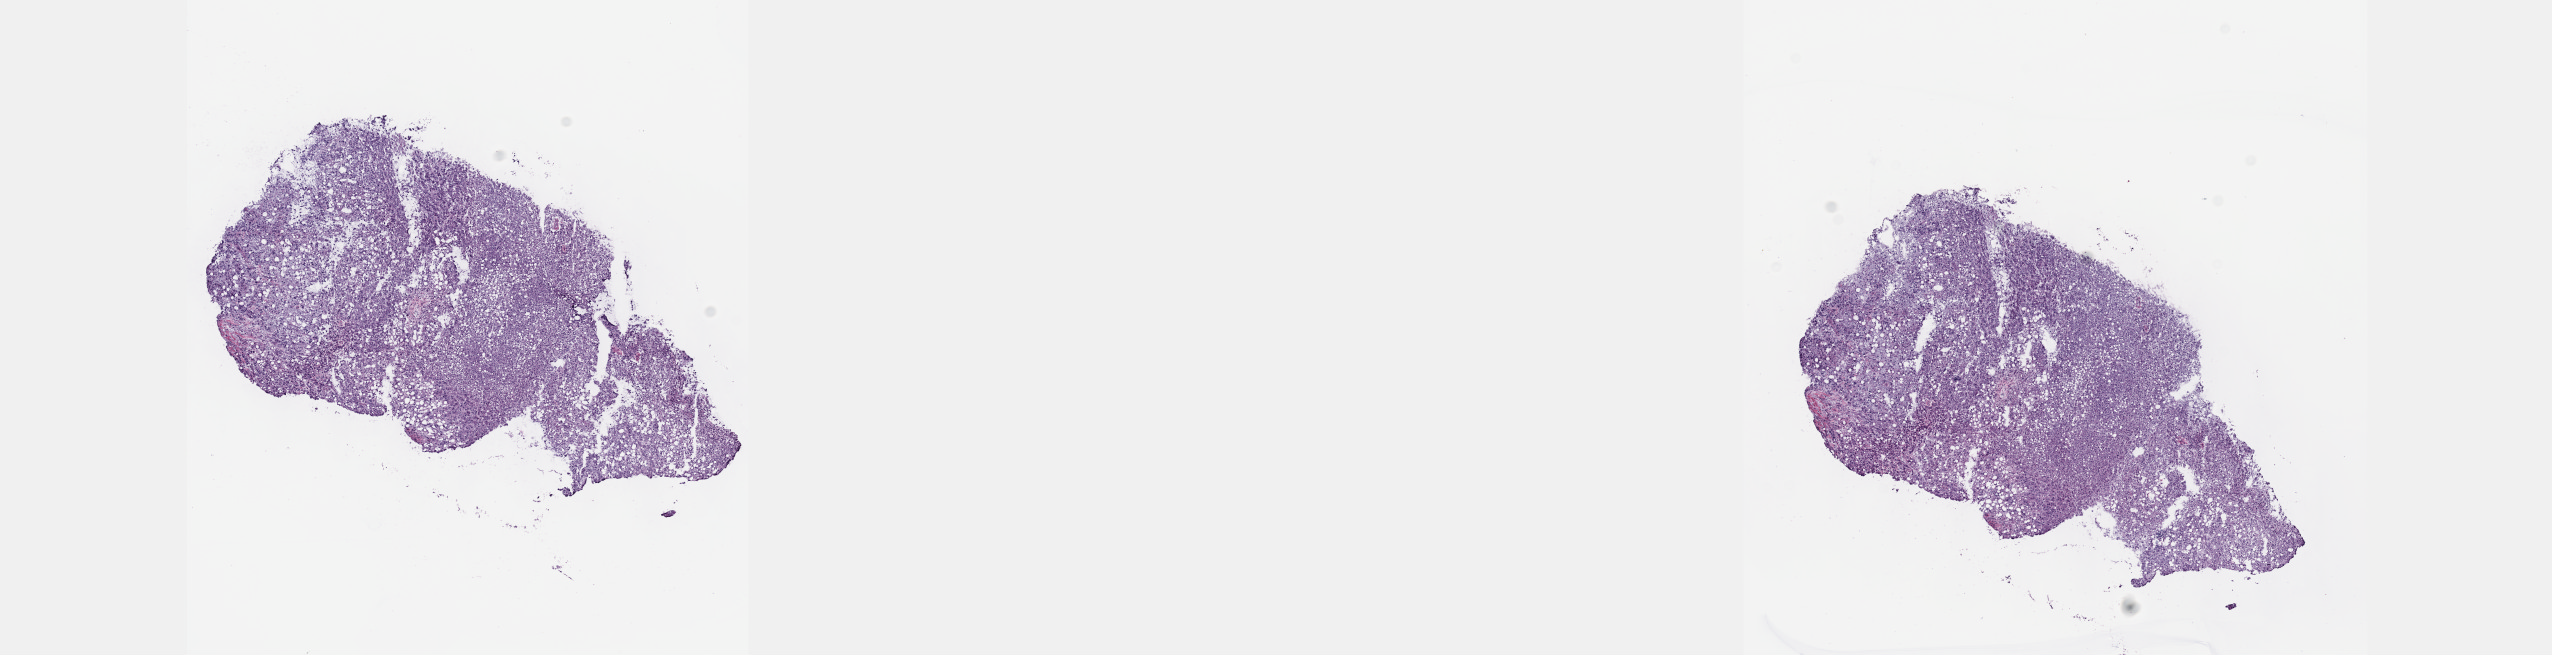
Whole-slide histology image, H&E-stained — whole scanned area (about 20.6 x 5.3 mm) shown as a low-resolution overview; frozen section; primary tumour sample from the liver. Patient: female, age at initial diagnosis 66 years. Histologic grade: G1 (well differentiated). Composition of this section per pathologist review: tumour cells 100%, tumour nuclei 85%, normal cells 0%, stromal cells 0%, necrosis 0%. Inflammatory infiltration, as recorded: lymphocyte infiltration 0%, monocyte infiltration 0%, neutrophil infiltration 0%.
Histologic diagnosis: Hepatocellular carcinoma, NOS.